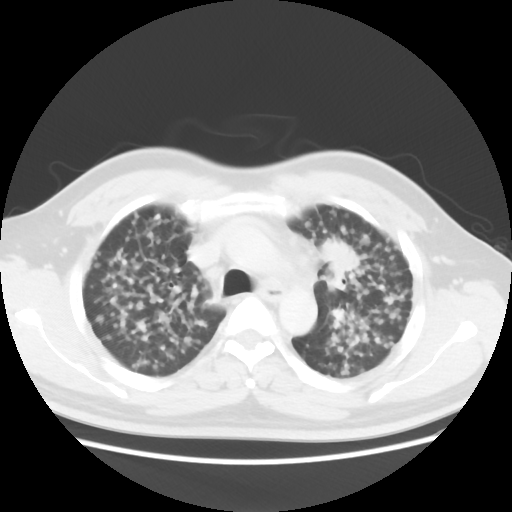
Chest CT, one axial slice; position 28 of 40 along the scan axis; reconstruction kernel STANDARD; 120 kVp; lung window (W 1500 / L -600 HU); 5 mm slice thickness; 512 × 512 image matrix, field of view 366 × 366 mm. Male patient, age 41 years. From the clinical record (not read from this slice): clinical TNM (as recorded): T1c N3 M1b.
Annotated regions visible in this slice (rectangle marked by the reading radiologist):
- lung tumour (recorded histology: adenocarcinoma): bounding box [x1, y1, x2, y2] px = [315, 238, 357, 284]